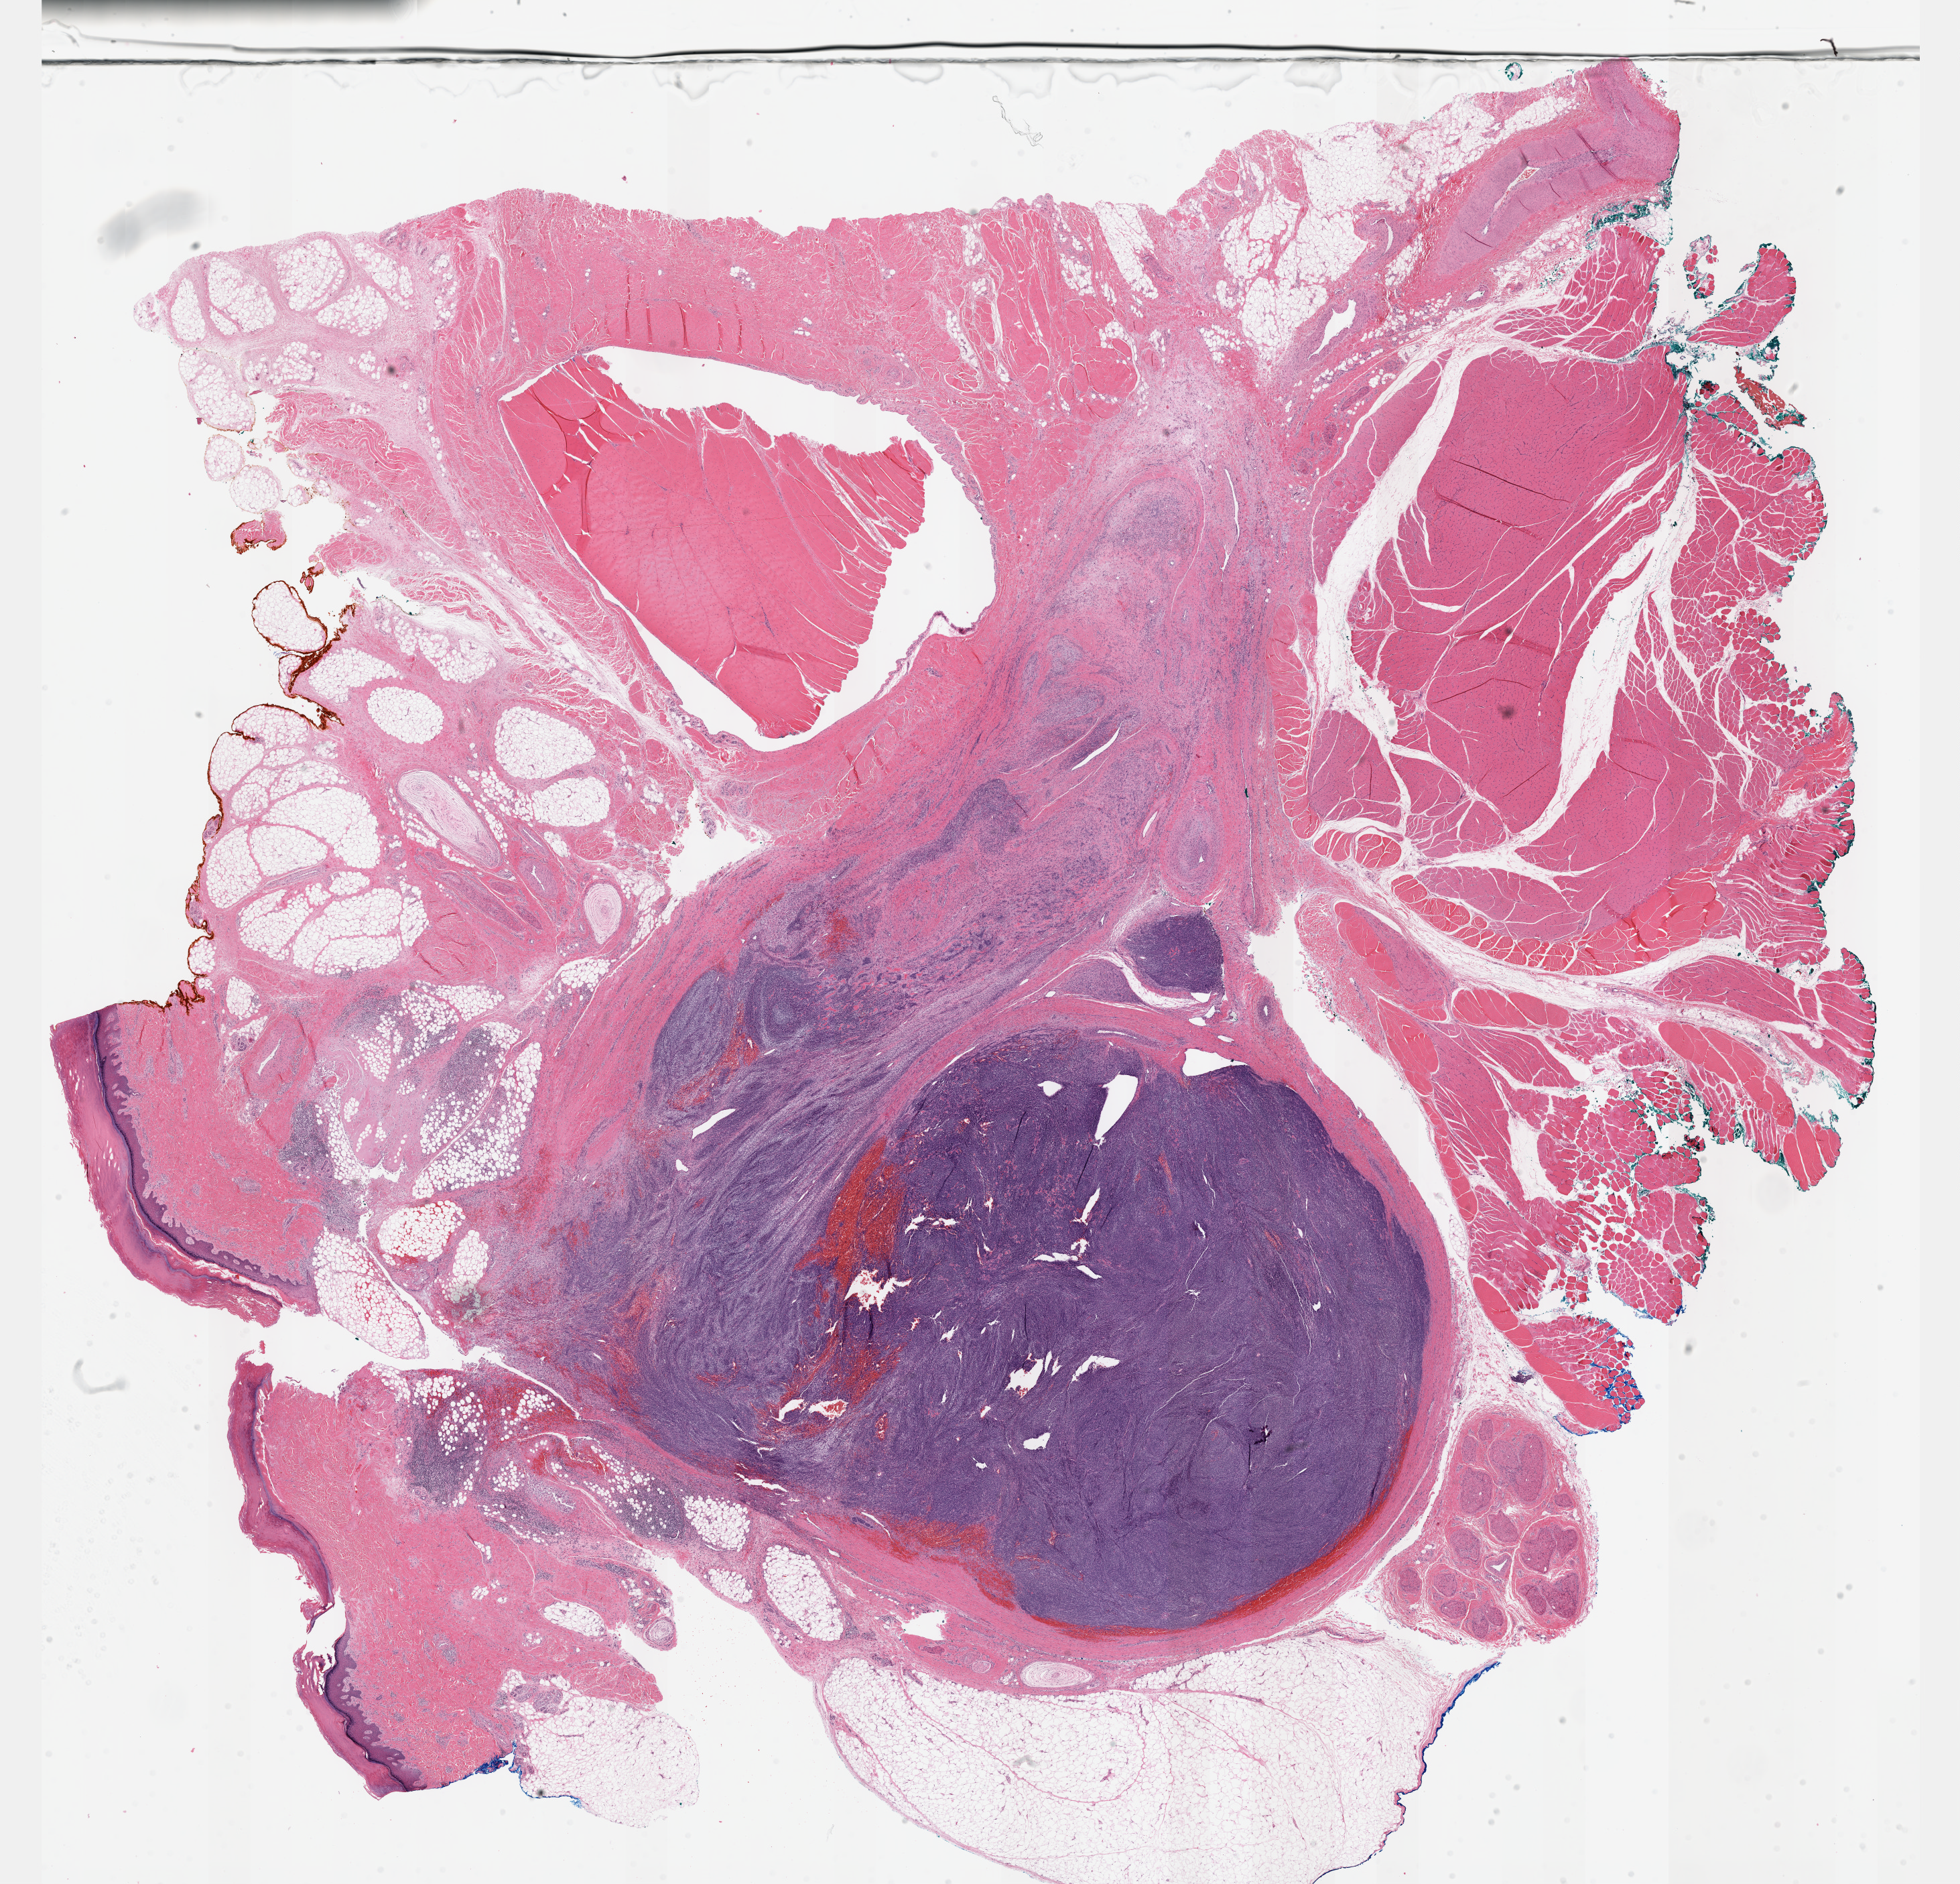
Whole-slide histology image, H&E-stained, low-resolution overview of the scanned area, about 23.6 x 22.7 mm. FFPE section. Connective, subcutaneous and other soft tissues, primary tumour sample. Patient: female, age at initial diagnosis 24 years.
Diagnosis: Synovial sarcoma, biphasic (connective, subcutaneous and other soft tissues of lower limb and hip).